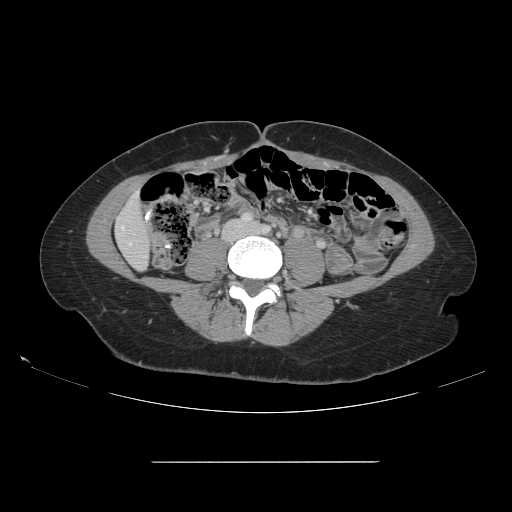
Contrast-enhanced abdominal CT, one axial slice; position 19 of 151 along the scan axis; soft-tissue window (W 400 / L 40 HU); 512 × 512 image matrix, field of view 421 × 421 mm. Female patient, age 46 years. Case-level facts recorded for this patient, not image findings: diagnosis: colorectal cancer liver metastases, imaged before liver resection; multiple liver metastases: yes; largest metastasis: 3 cm; chemotherapy before resection: no.
Outlined on this slice (expert manual segmentation):
- liver: bounding box [x1, y1, x2, y2] px = [117, 197, 150, 269]
- planned liver remnant (the part of the liver to remain after resection): [117, 197, 150, 269]